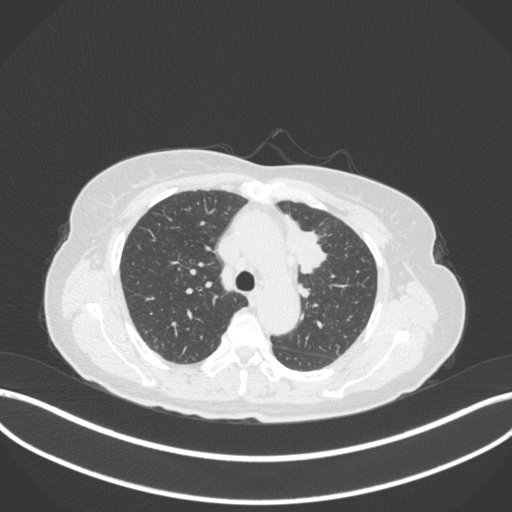
Chest CT, one axial slice. Position 237 of 368 along the scan axis. Reconstruction kernel B31f. 120 kVp. Lung window (W 1500 / L -600 HU). 512 × 512 image matrix. Female patient, age 65 years. From the clinical record (not read from this slice): clinical TNM (as recorded): T2a N0 M0; histopathological grade: G2-3.
Structures marked on this image (rectangle marked by the reading radiologist):
- lung tumour (recorded histology: adenocarcinoma): bounding box <281,215,331,276> (left, top, right, bottom; pixels)